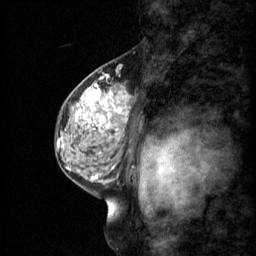
Breast MRI (dynamic contrast-enhanced), one sagittal slice; 3 images stored at this slice position (order not interpretable as contrast timing); 1.5 T; TE 4.2 ms, TR 11 ms; 2 mm slice thickness; 256 × 256 image matrix, field of view 200 × 200 mm. Female patient, age 48 years.
Structures marked on this image (semi-automatic segmentation, software-assisted and operator-edited):
- analysis volume of interest (the breast-tissue region the enhancement analysis was run in; not a lesion): bounding box (x1, y1, x2, y2) in pixels: (69, 74, 134, 147)
- tumour enhancement mask (voxels above the 70 % enhancement threshold inside the analysis volume of interest): (76, 84, 129, 141)